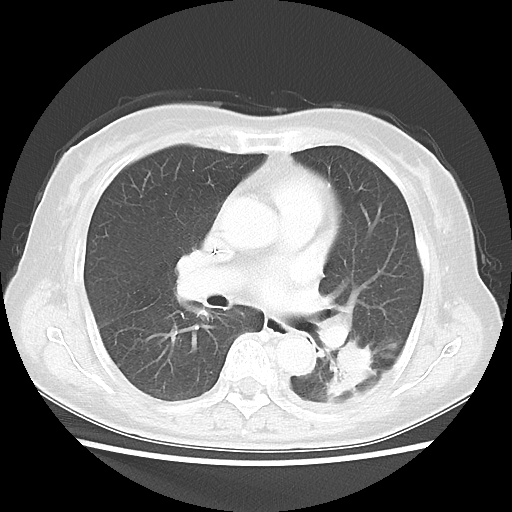
Chest CT, one axial slice; position 20 of 40 along the scan axis; reconstruction kernel LUNG; 100 kVp; lung window (W 1500 / L -600 HU); 5 mm slice thickness; 512 × 512 image matrix, field of view 341 × 341 mm. Female patient, age 69 years. Case-level facts recorded for this patient, not image findings: clinical TNM (as recorded): T1c N0 M0.
Structures marked on this image (bounding box drawn by a radiologist):
- lung tumour (recorded histology: adenocarcinoma): box from (x=325, y=342) to (x=379, y=405) px